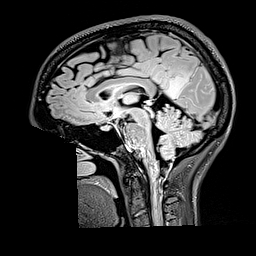
Brain MRI from a brain-tumour surgery series, one sagittal slice. Position 87 of 176 along the scan axis. T2 FLAIR. 1 mm slice thickness. 256 × 256 image matrix, field of view 256 × 256 mm. From the clinical record (not read from this slice): histopathology: Oligodendroglioma; WHO grade: 2; IDH mutation: yes; tumour location: Right Parietal.
Annotated regions visible in this slice (outlined manually by an expert reader):
- tumour: bounding box [x1, y1, x2, y2] px = [165, 73, 190, 98]